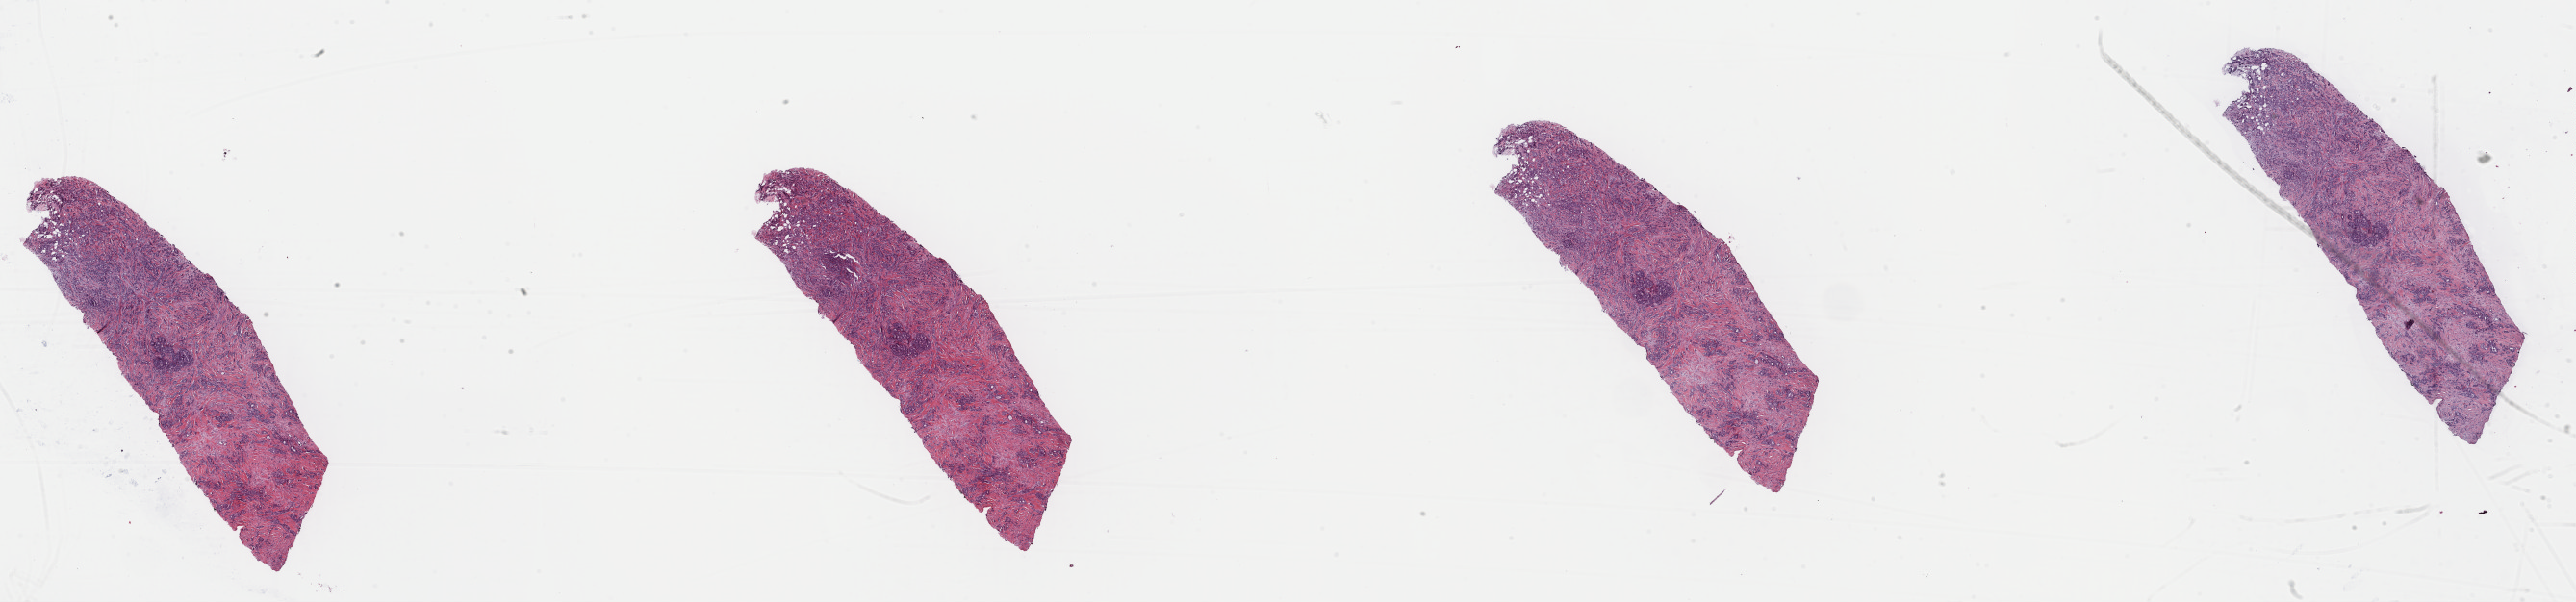
Hematoxylin and eosin (H&E) stained whole-slide image — low-resolution overview of the scanned area, about 42.2 x 9.9 mm; FFPE section; primary tumour sample from the breast. Female, age 56 years at initial diagnosis.
Lymph nodes positive (case pathology): 0 of 4 examined. Histologic diagnosis: Infiltrating duct carcinoma, NOS. AJCC pathologic stage: IIA.